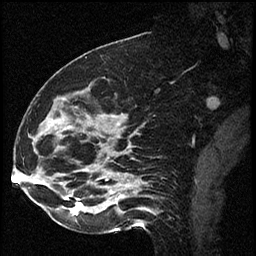
Breast MRI (dynamic contrast-enhanced), one sagittal slice. Position 26 of 60 along the scan axis. Dynamic contrast-enhanced series, image 2 of 2 at this slice position (ordered by acquisition). 1.5 T. TE 4.2 ms, TR 17.3 ms. 2 mm slice thickness. 256 × 256 image matrix, field of view 200 × 200 mm. Female patient. Case-level facts recorded for this patient, not image findings: setting: breast cancer imaged before/during neoadjuvant chemotherapy; receptor status: HR-positive, HER2-negative.
Outlined on this slice (semi-automatically segmented with operator editing):
- analysis volume of interest (the breast-tissue region the enhancement analysis was run in; not a lesion): box from (x=41, y=93) to (x=115, y=223) px
- tumour enhancement mask (voxels above the 100 % enhancement threshold inside the analysis volume of interest): (x=72, y=199)–(x=82, y=214)